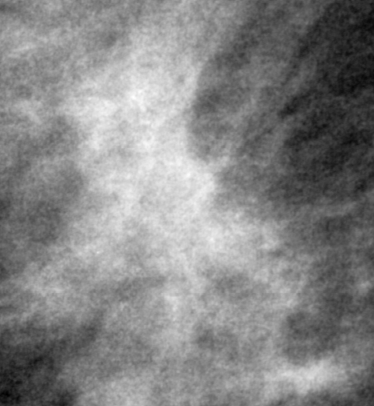
Cropped region of a digitized screen-film mammogram centred on a radiologist-marked abnormality, left breast, MLO view, BI-RADS breast density category 2 (scale 1–4).
- Finding: mass, shape irregular, margins spiculated; BI-RADS assessment category 5; subtlety rating 5 on a 1 (subtle) to 5 (obvious) scale; pathology (as recorded): malignant.